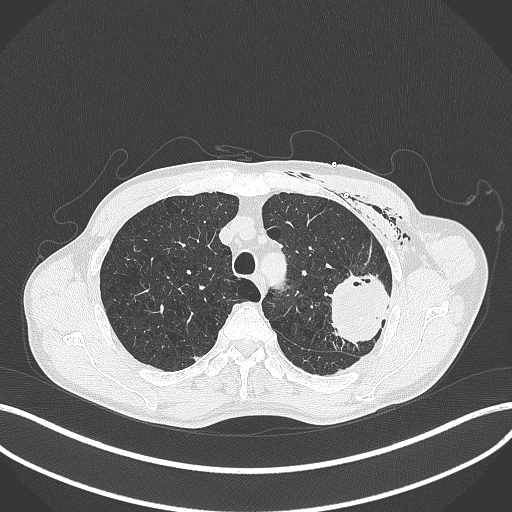
Chest CT, one axial slice. Slice 316 of 457 in the series (ordered by position). 120 kVp. Lung window (W 1500 / L -600 HU). 512 × 512 image matrix, field of view 400 × 400 mm. Male patient, age 58 years. From the clinical record (not read from this slice): clinical TNM (as recorded): T3 N0 M0.
Outlined on this slice (bounding box drawn by a radiologist):
- lung tumour (recorded histology: adenocarcinoma): bounding box [x1, y1, x2, y2] px = [320, 271, 393, 346]